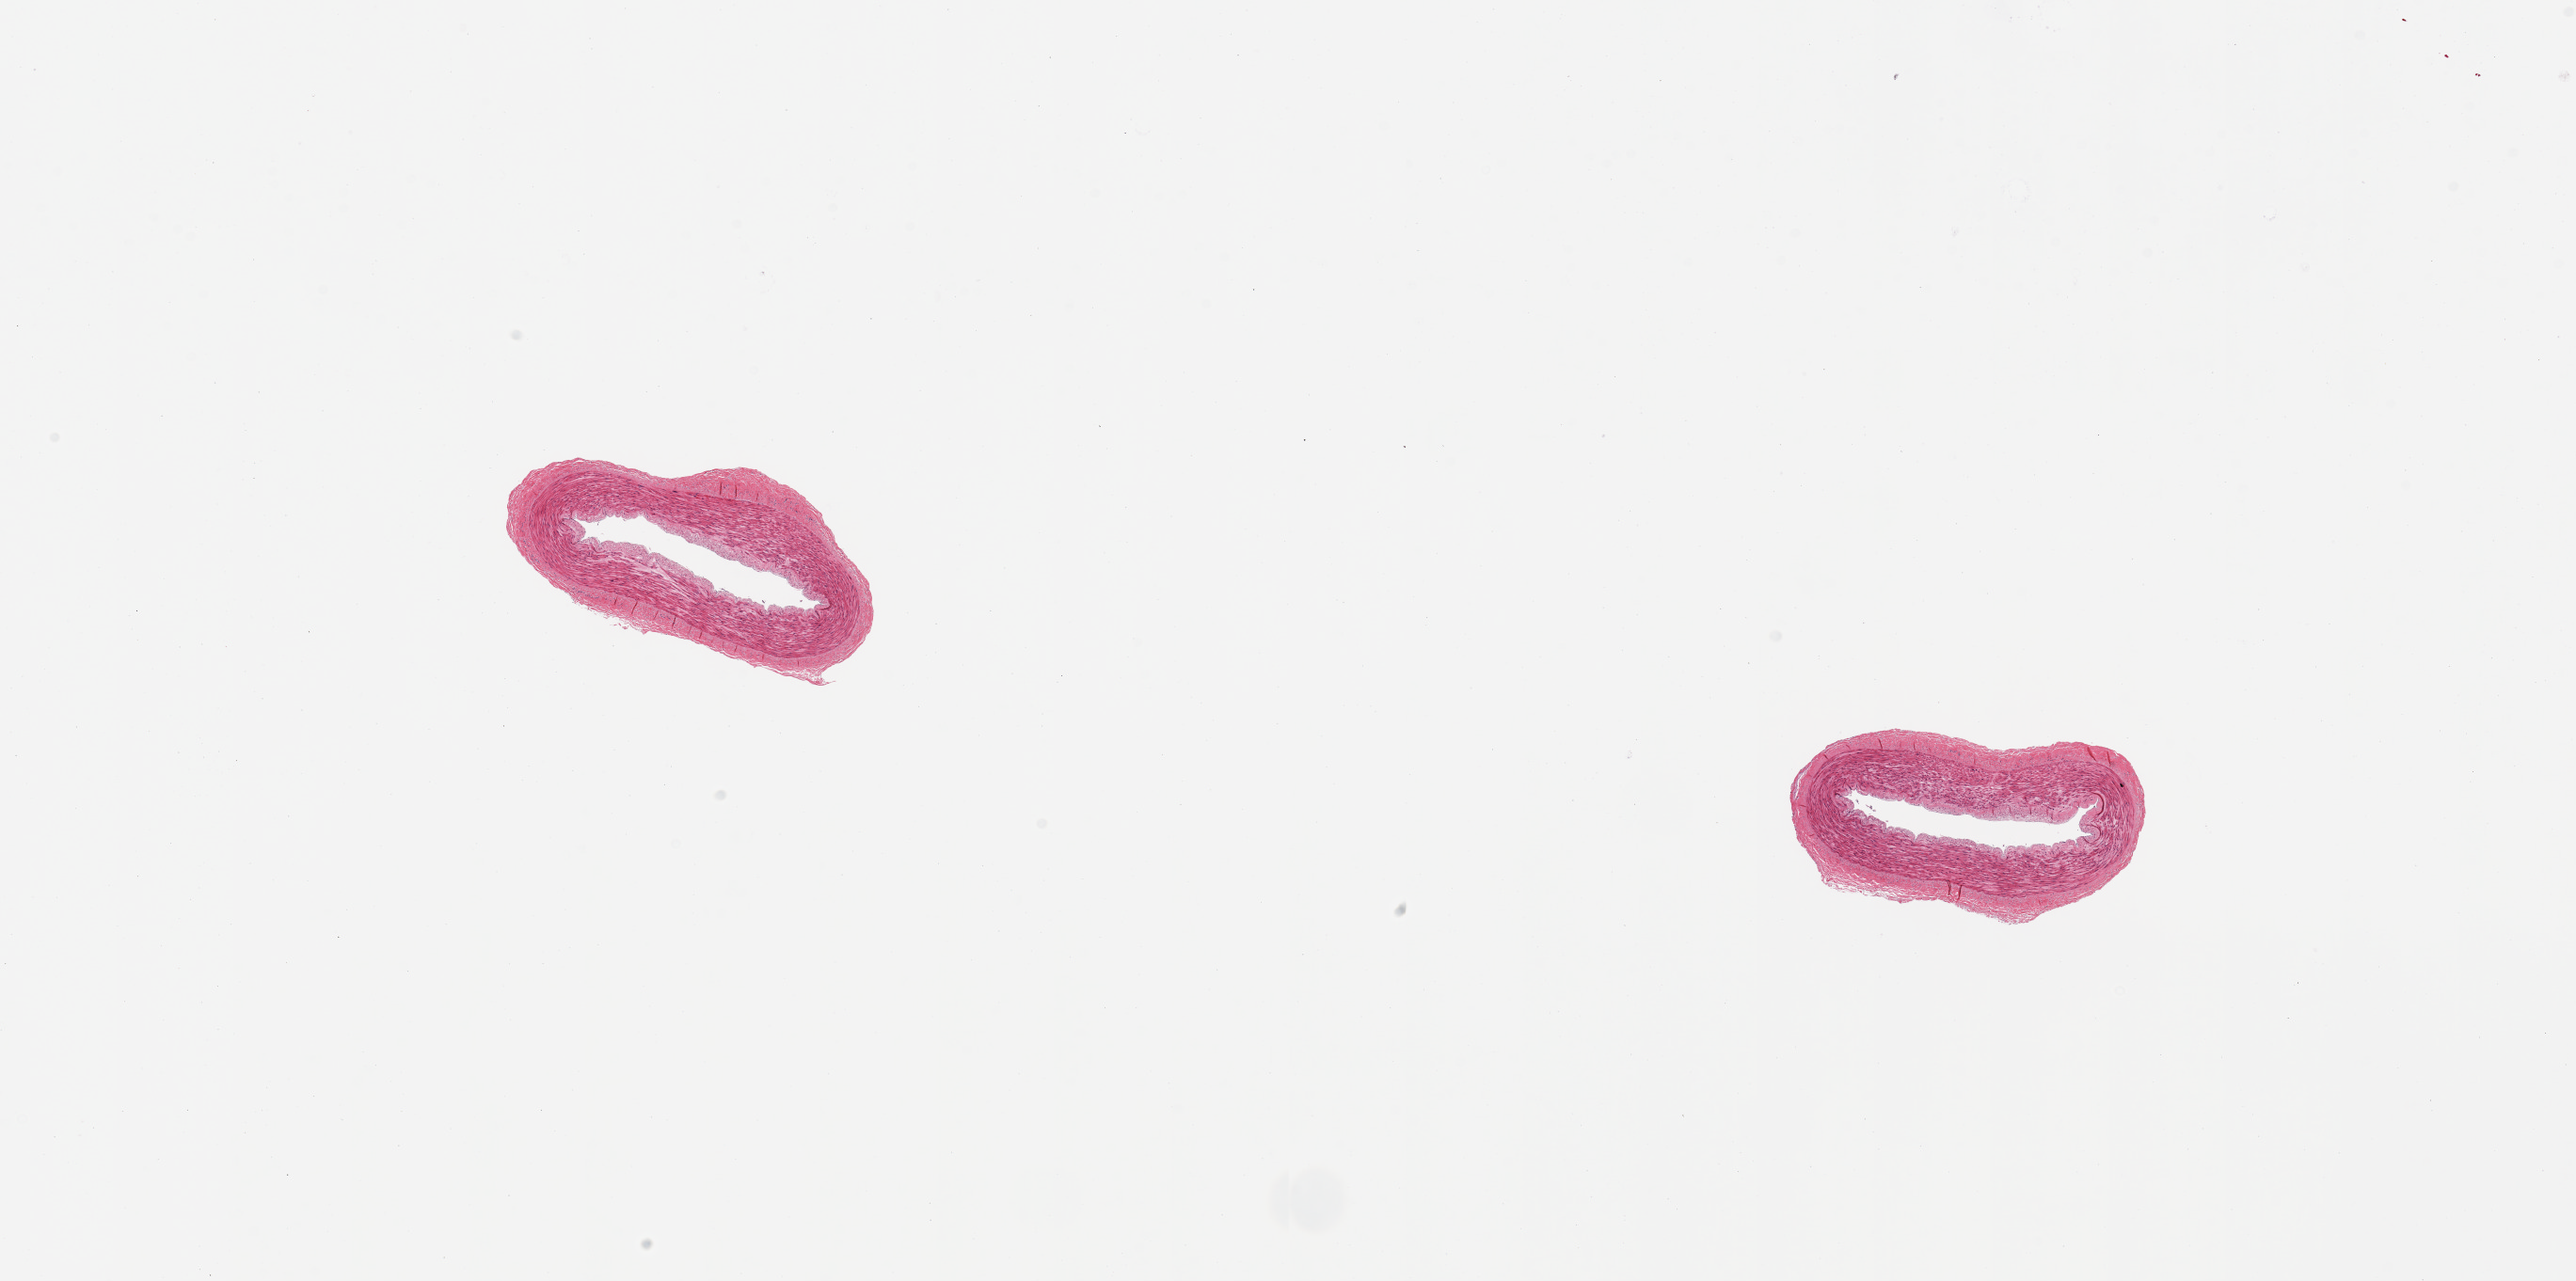
Whole-slide image, haematoxylin and eosin stain, shown as a low-resolution overview of the whole scanned area (about 21.7 x 10.8 mm, from a 20x scan), PAXgene-fixed paraffin-embedded (PFPE) section, target tissue: tibial artery, tissue donor sample. Donor: male.
Pathologist's review note for this sample: 2 pieces; well trimmed.